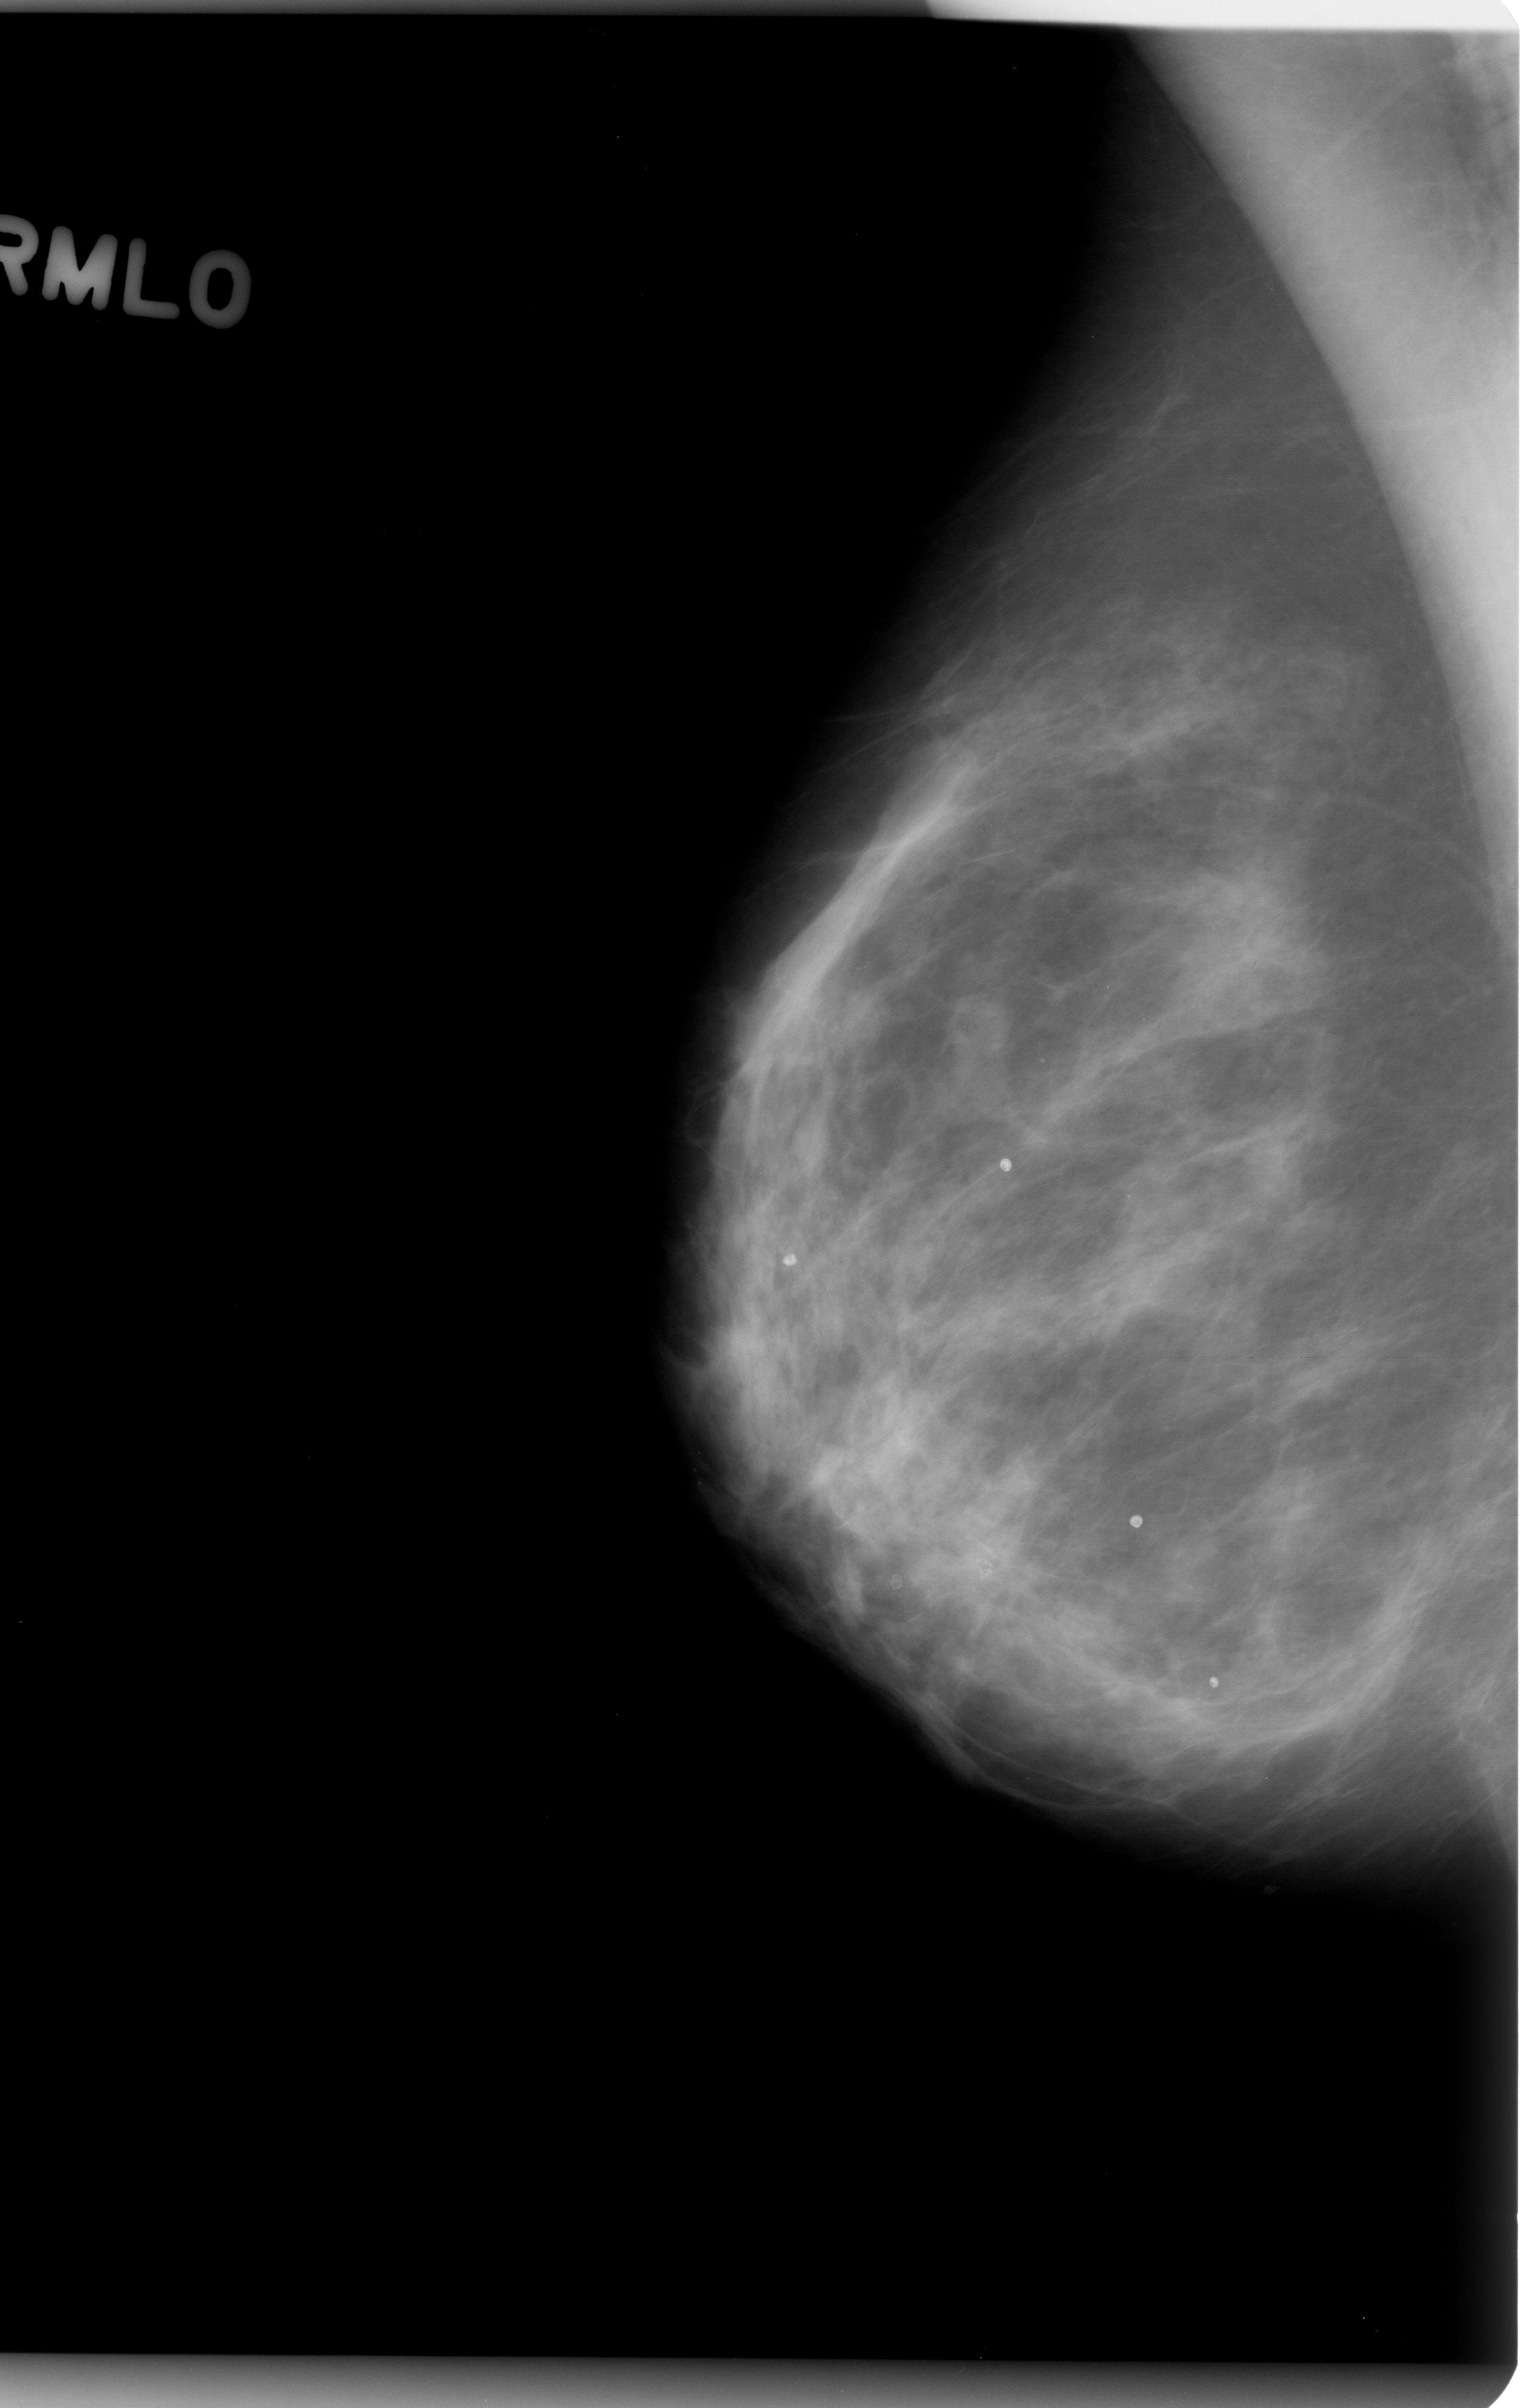
Scanned film-screen mammogram, right breast, MLO view, breast composition: scattered fibroglandular densities (BI-RADS density category 2 of 4).
Marked findings (only marked abnormalities are described; nothing is implied about the rest of the image): mass, shape round, margins obscured; BI-RADS assessment category 3; pathology result (as recorded, not read from the image): benign.